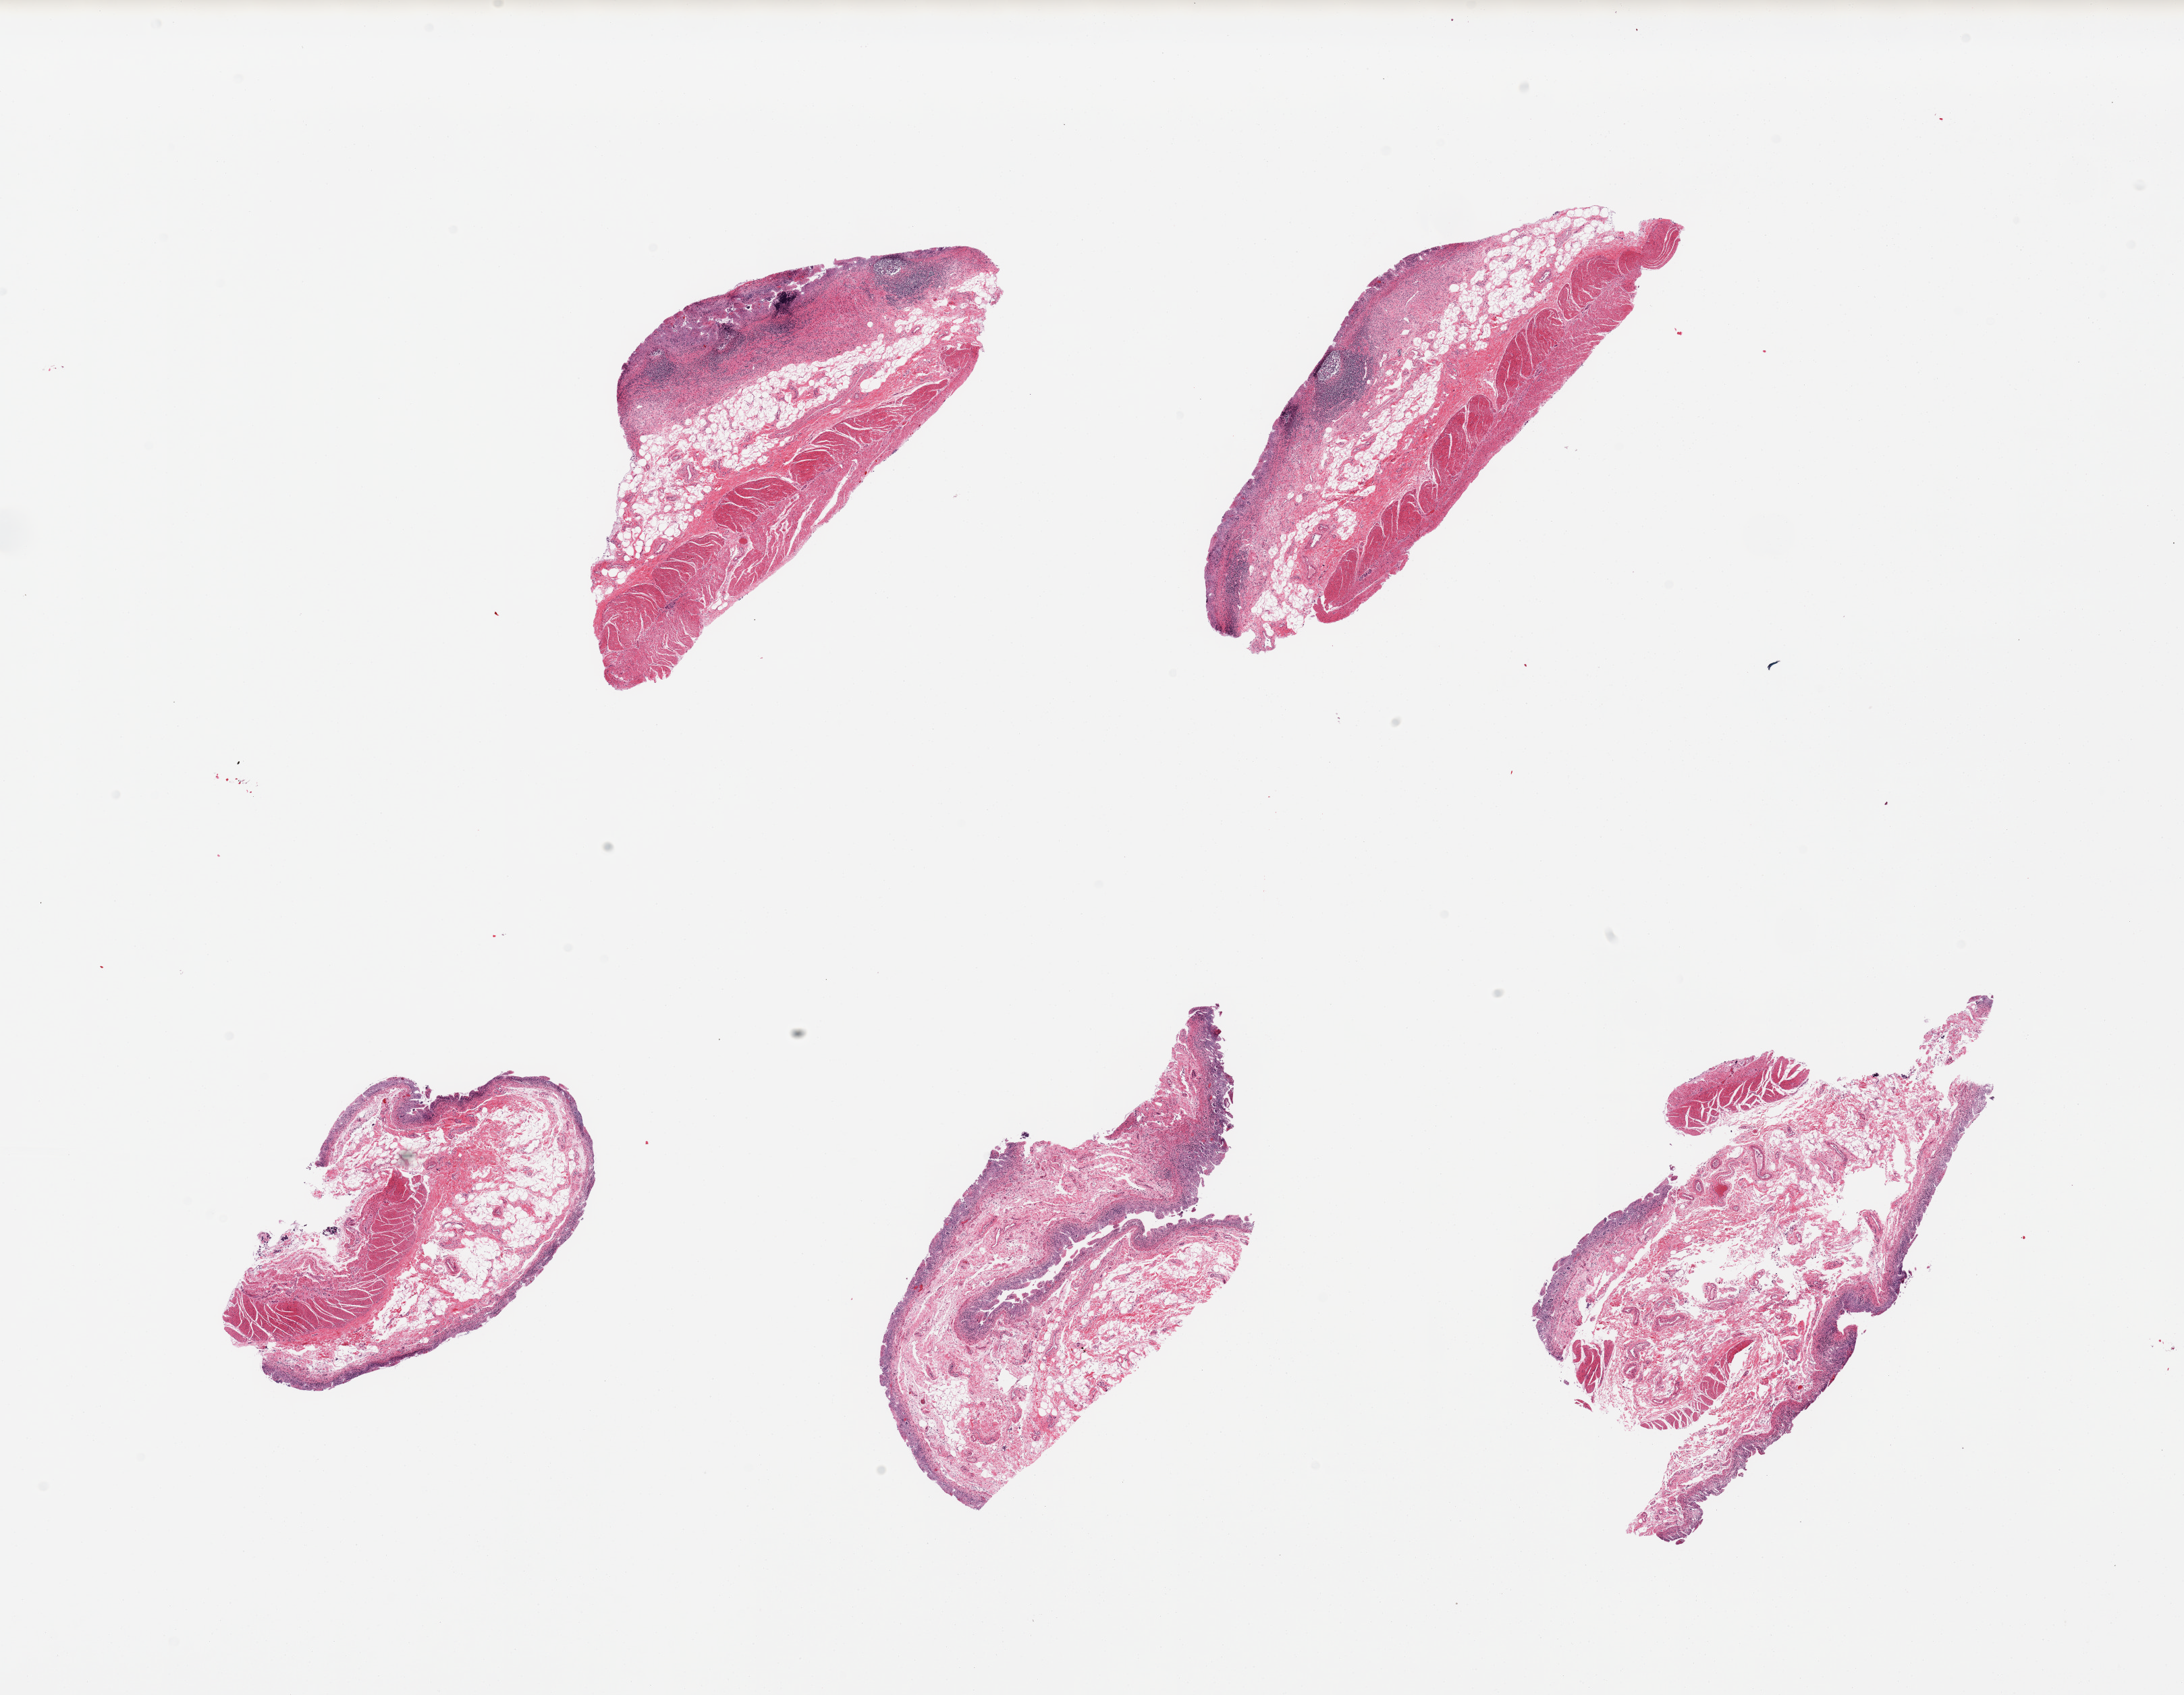
Digitized hematoxylin and eosin (H&E)-stained section, shown as a low-resolution overview of the whole scanned area (about 25.6 x 19.9 mm, from a 20x scan), PAXgene-fixed, paraffin-embedded tissue, section of ileum (target tissue), tissue donor sample. Donor sex: male.
* pathologist's review note for this sample: 6 pieces, marked autolysia; lymphoid component is ~20% total